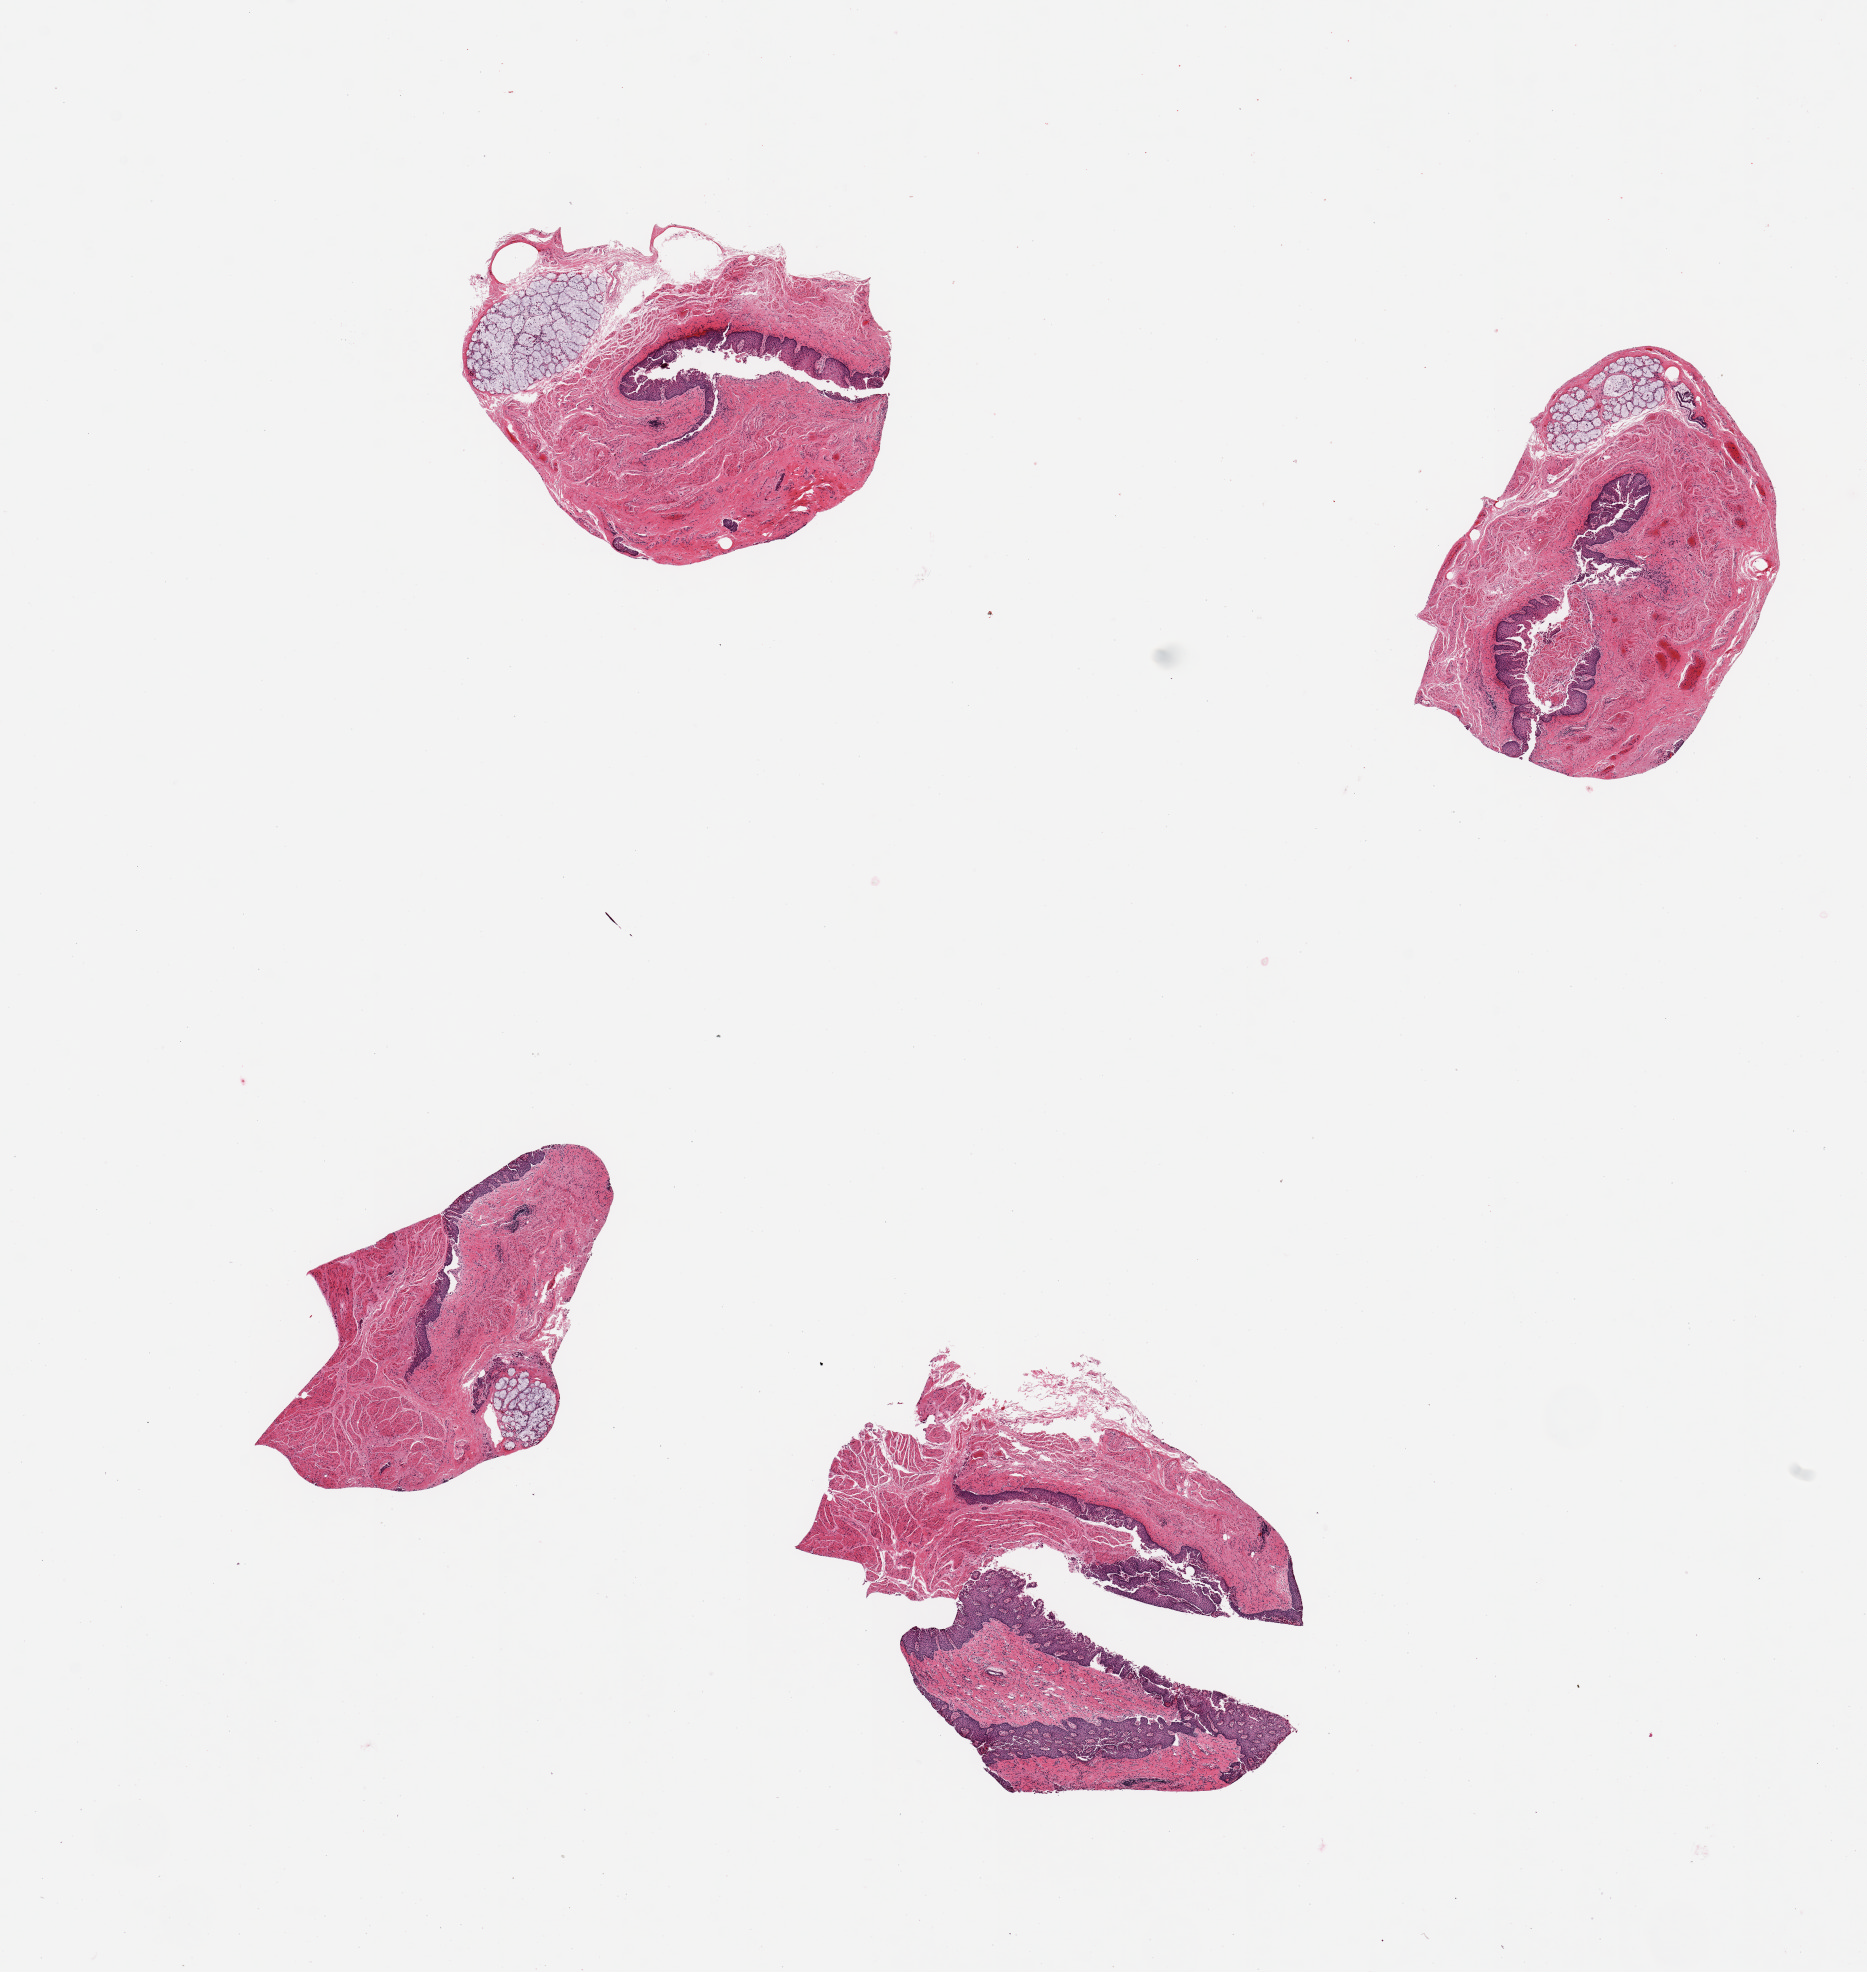
Whole-slide image, H&E stain — a low-resolution overview of the entire scanned area, about 14.8 x 15.6 mm (from a 20x scan). PAXgene-fixed paraffin-embedded (PFPE) section. Section of esophageal mucous membrane (target tissue). Donor tissue sample. Donor sex: female.
Pathologist's review note for this sample: 4 pieces; submucosal glands in three pieces.